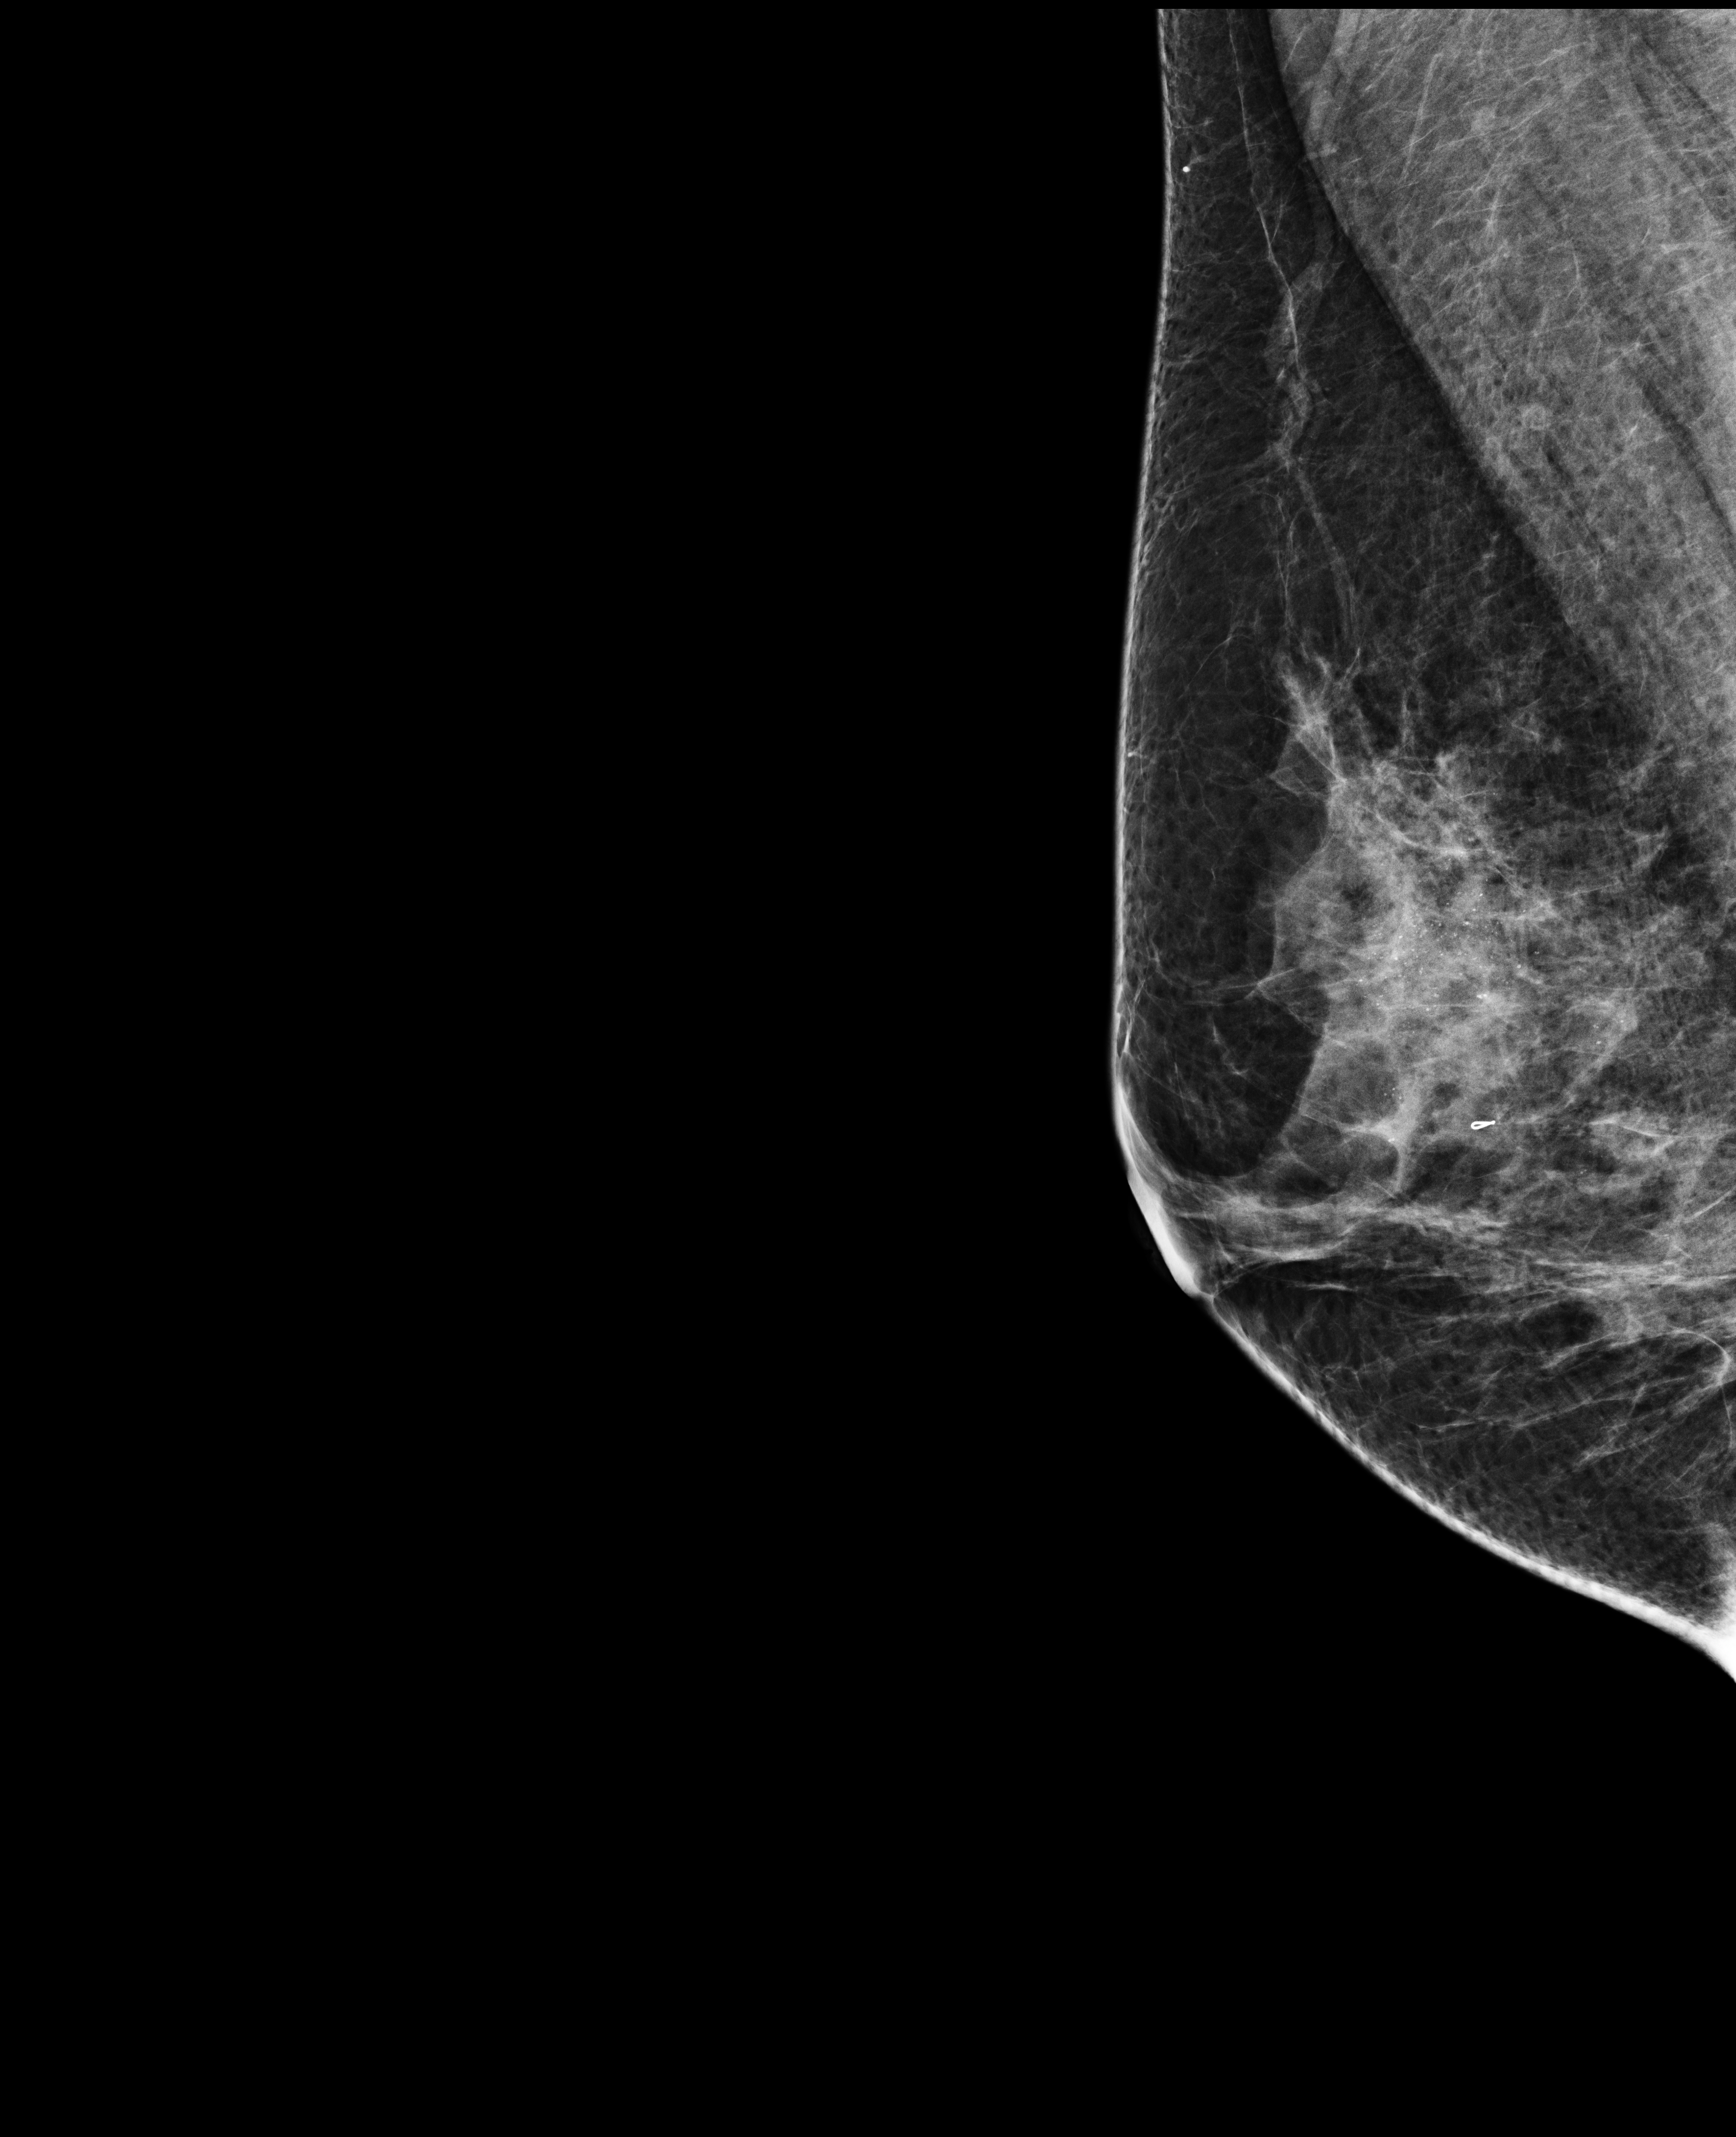
Screening examination, system: Selenia Dimensions. Patient aged 49 years (female).
Image type: full-field digital mammogram. Breast: right. Projection: medio-lateral oblique projection.